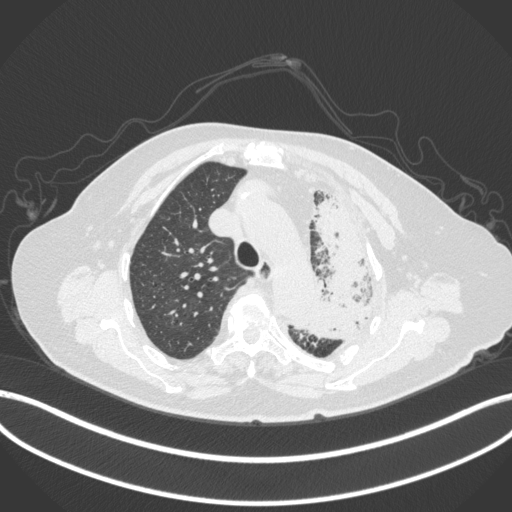
Chest CT, one axial slice. Reconstruction kernel B31f. 120 kVp. Lung window (W 1500 / L -600 HU). 1 mm slice thickness. 512 × 512 image matrix, field of view 400 × 400 mm. Patient: female, 75 years. Case-level facts recorded for this patient, not image findings: clinical TNM (as recorded): T3 N3 M1.
Outlined on this slice (bounding box drawn by a radiologist):
- lung tumour (recorded histology: adenocarcinoma): bounding box (x1, y1, x2, y2) in pixels: (291, 194, 387, 343)